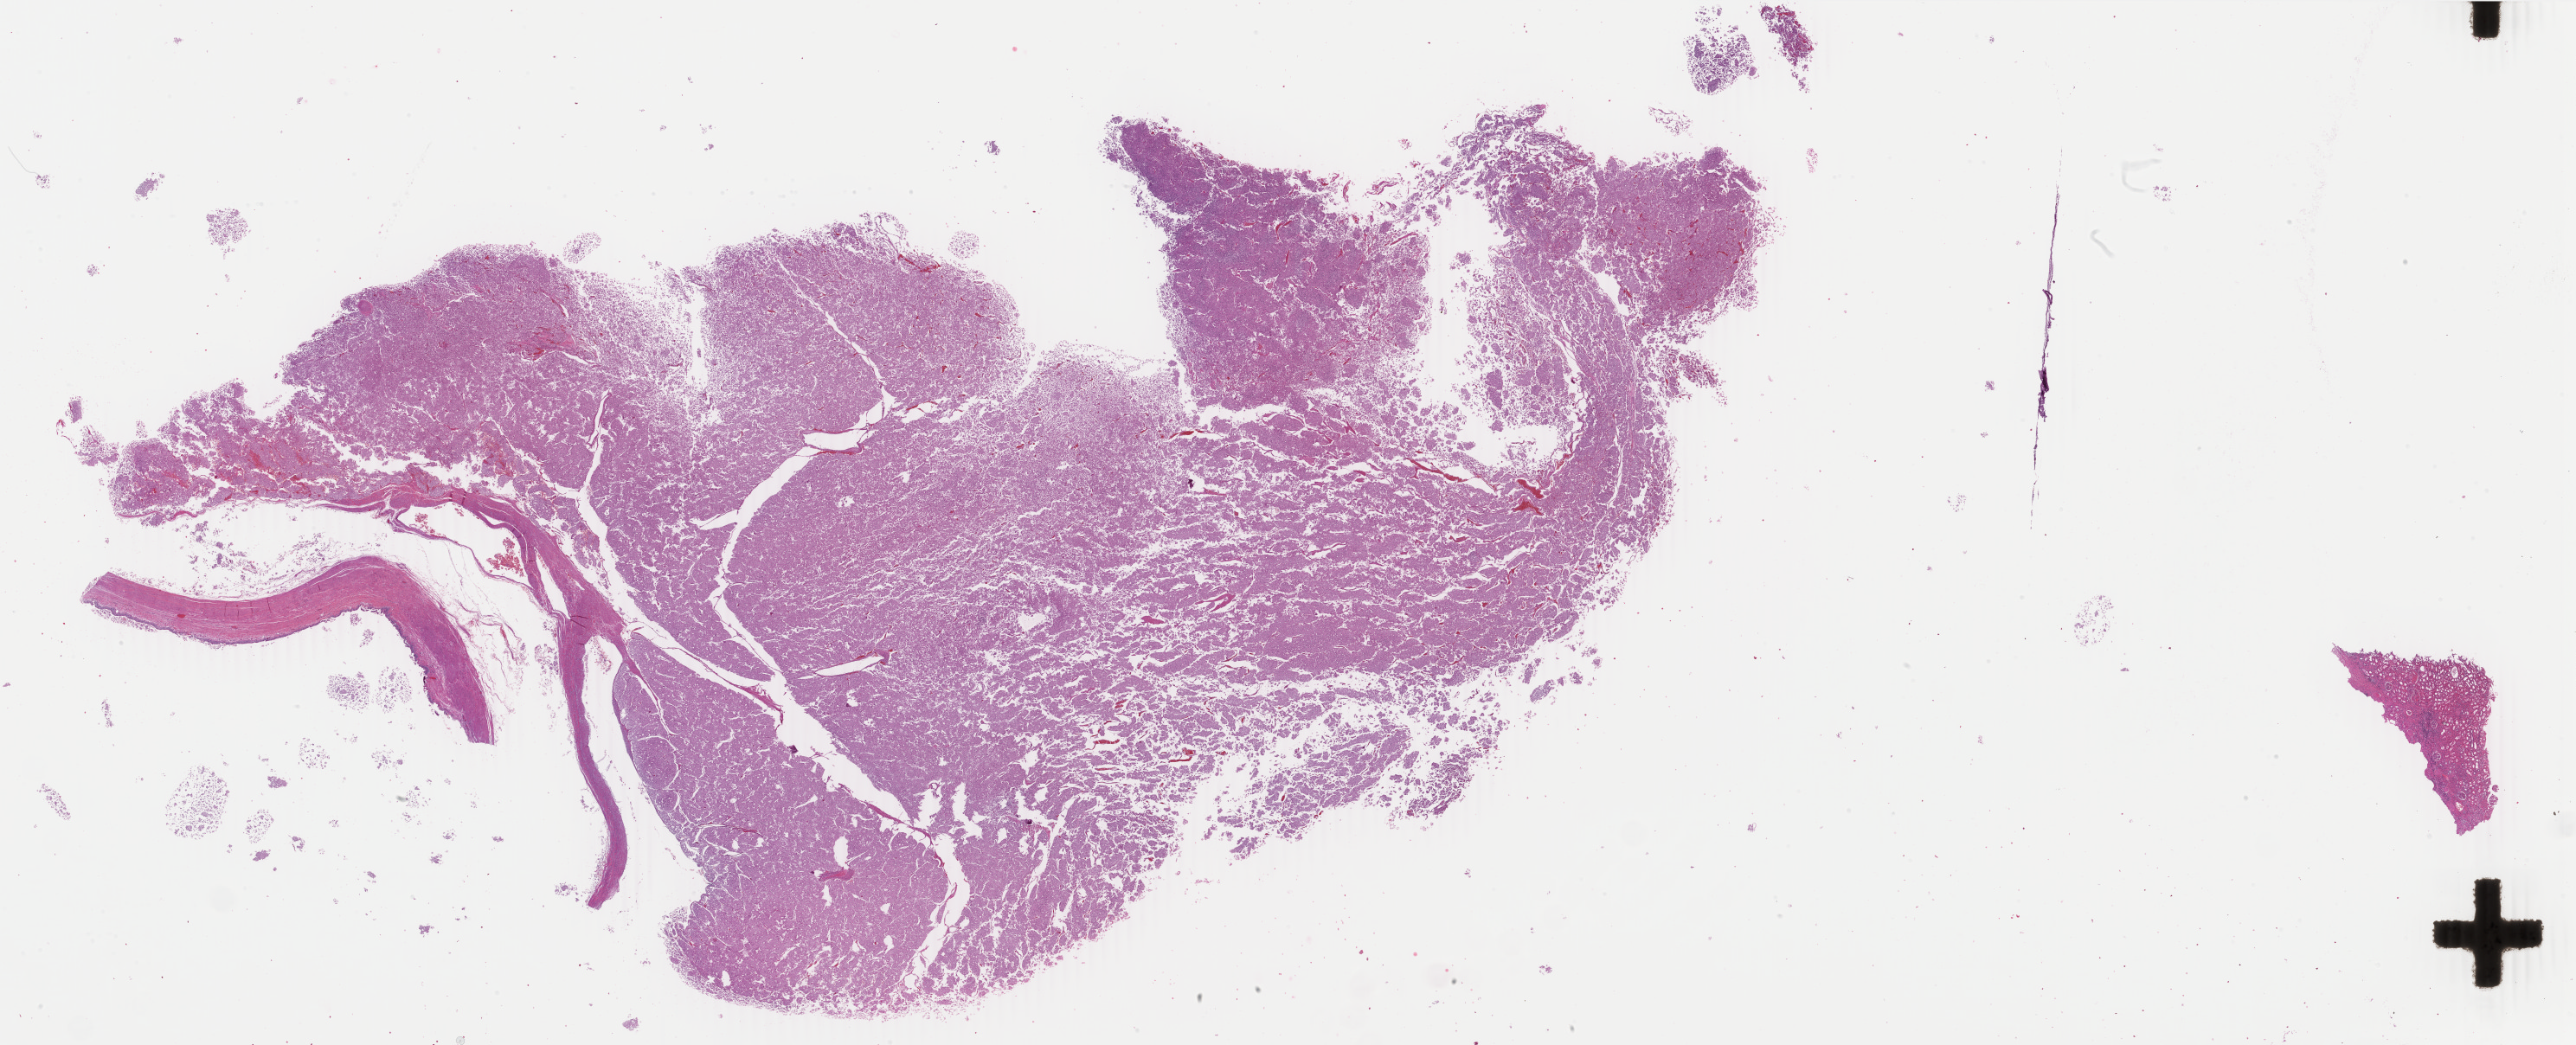
Whole-slide histology image, H&E — a low-resolution overview of the entire scanned area, about 47.4 x 19.2 mm (acquisition: 40x scan). FFPE section. Primary tumour sample from the kidney. Male, age 37 years at initial diagnosis.
Pathologic diagnosis: Renal cell carcinoma, chromophobe type.